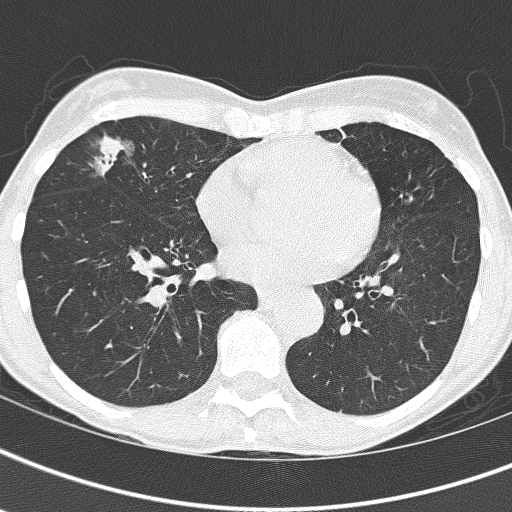
Chest CT (low-dose screening protocol), one axial image. First (baseline) screen. Lung window (W 1500 / L -600 HU). Lung (sharp) reconstruction kernel (B60f). Slice 97 of 161 in the series. 512 × 512 image matrix. Female, age 67 years at enrolment.
- Lesion marked by an expert reader, box from (x=86, y=126) to (x=178, y=207) px.
- No non-calcified nodule or mass ≥4 mm was recorded by the screening reader at this exam.
- Official screen result: negative screen, significant abnormalities not suspicious for lung cancer.
- Later outcome: lung cancer diagnosed 832 days after this screen (after the third annual screen) — bronchiolo-alveolar adenocarcinoma, NOS, right middle lobe, well differentiated (G1), stage IA (AJCC 6th edition), 25 mm at pathology.